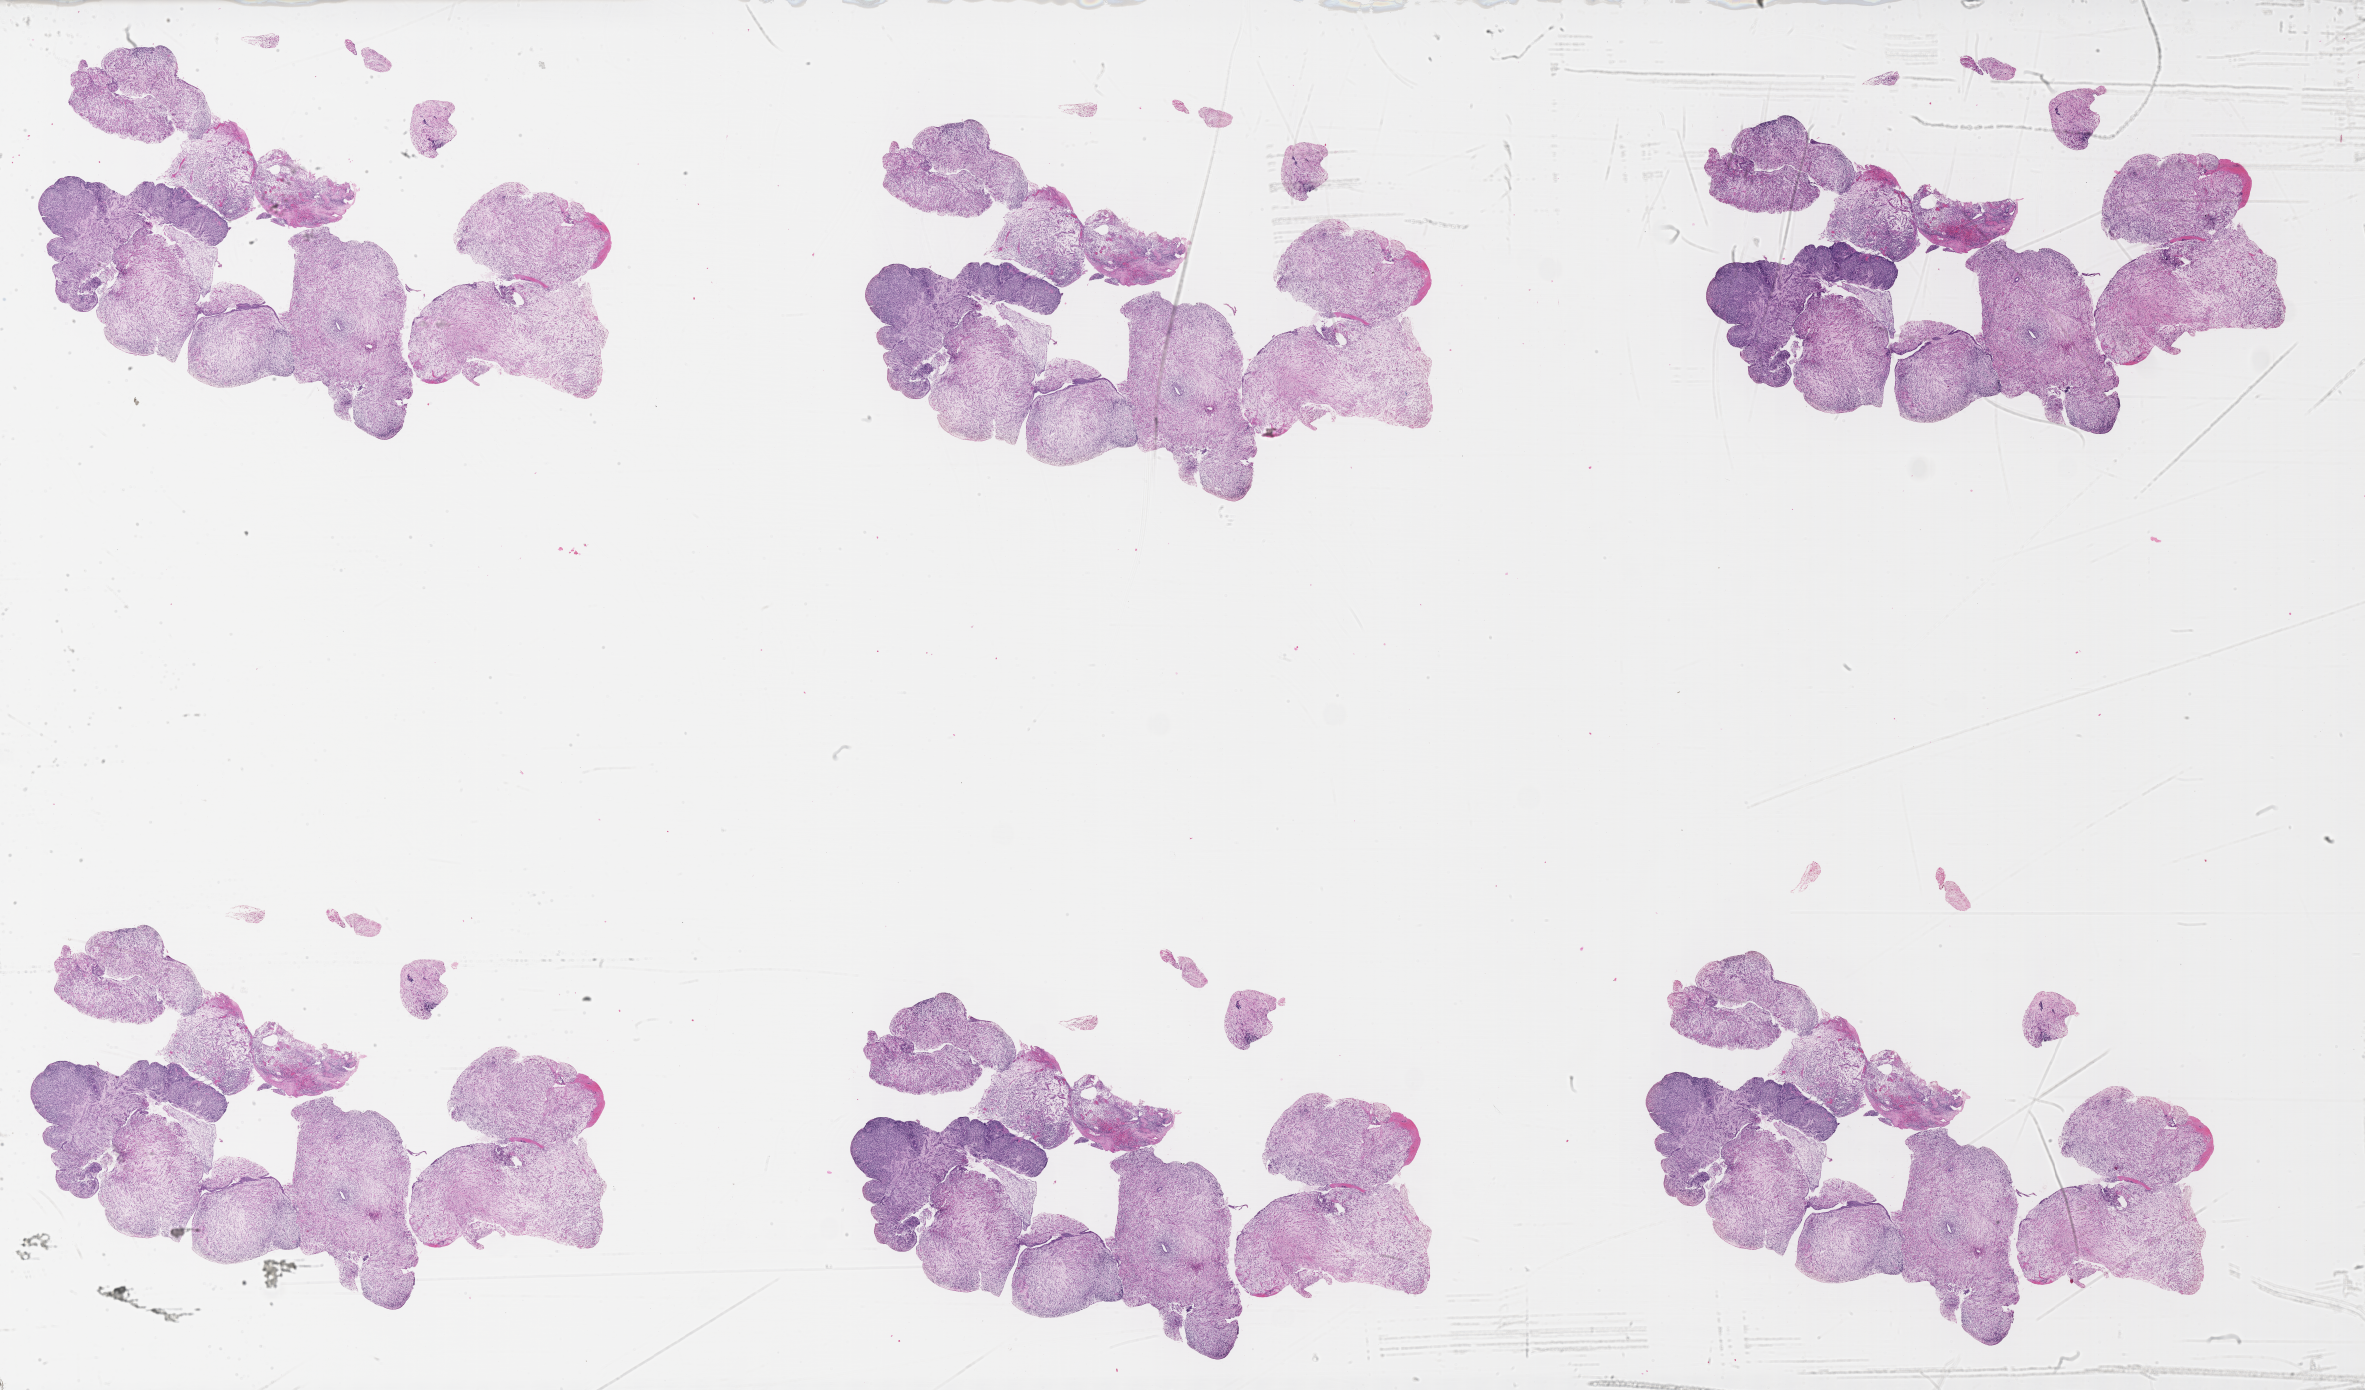
Whole-slide image, H&E stain of tumor tissue, a low-resolution overview of the entire scanned area, about 38.2 x 22.5 mm, formalin-fixed, paraffin-embedded (FFPE) tissue, sample anatomic site: prostate. Male patient, age at diagnosis 1.7 years.
Metastatic status at presentation (as recorded): non-metastatic (confirmed). Diagnosis: rhabdomyosarcoma; histological classification: embryonal rhabdomyosarcoma. Stage (as recorded): 2.